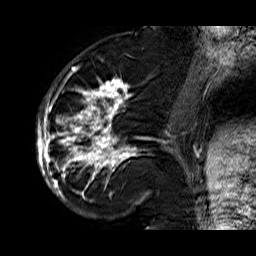
Breast MRI (dynamic contrast-enhanced), one sagittal slice; position 23 of 60 along the scan axis; dynamic contrast-enhanced series, time point 2 of 6 at this slice position (early post-contrast); 1.5 T; TE 6.3 ms, TR 32.9 ms; 256 × 256 image matrix, field of view 200 × 200 mm. Female patient. From the clinical record (not read from this slice): setting: breast cancer imaged before/during neoadjuvant chemotherapy; receptor status: HR-positive, HER2-negative.
Annotated regions visible in this slice (semi-automatically segmented with operator editing):
- analysis volume of interest (the breast-tissue region the enhancement analysis was run in; not a lesion): box from (x=36, y=74) to (x=176, y=210) px
- tumour enhancement mask (voxels above the 100 % enhancement threshold inside the analysis volume of interest): (x=36, y=75)–(x=174, y=202)